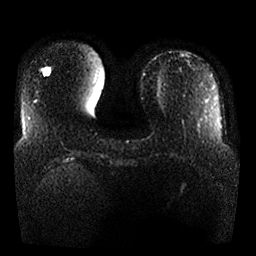
Breast MRI, one axial slice; slice 5 of 25 in the series (ordered by position); diffusion-weighted series; image 2 of 4 stored at this slice position (different b-values; order by instance number); 1.5 T; 4 mm slice thickness; 256 × 256 image matrix, field of view 360 × 360 mm. Female patient.
Outlined on this slice (manually delineated by an expert):
- tumour on diffusion-weighted imaging: bounding box (x1, y1, x2, y2) in pixels: (46, 70, 49, 74)